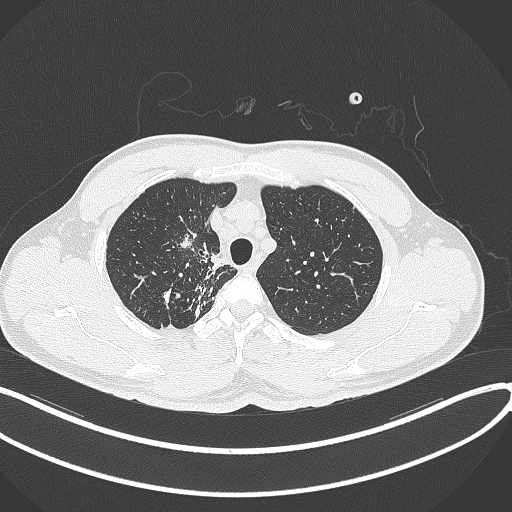
Chest CT, one axial slice. Position 302 of 391 along the scan axis. Reconstruction kernel B70f. Lung window (W 1500 / L -600 HU). 1 mm slice thickness. 512 × 512 image matrix, field of view 400 × 400 mm. Male patient, age 48 years. Case-level facts recorded for this patient, not image findings: clinical TNM (as recorded): T1c N1 M1.
Outlined on this slice (rectangle marked by the reading radiologist):
- lung tumour (recorded histology: adenocarcinoma): bounding box (x1, y1, x2, y2) in pixels: (174, 225, 204, 263)